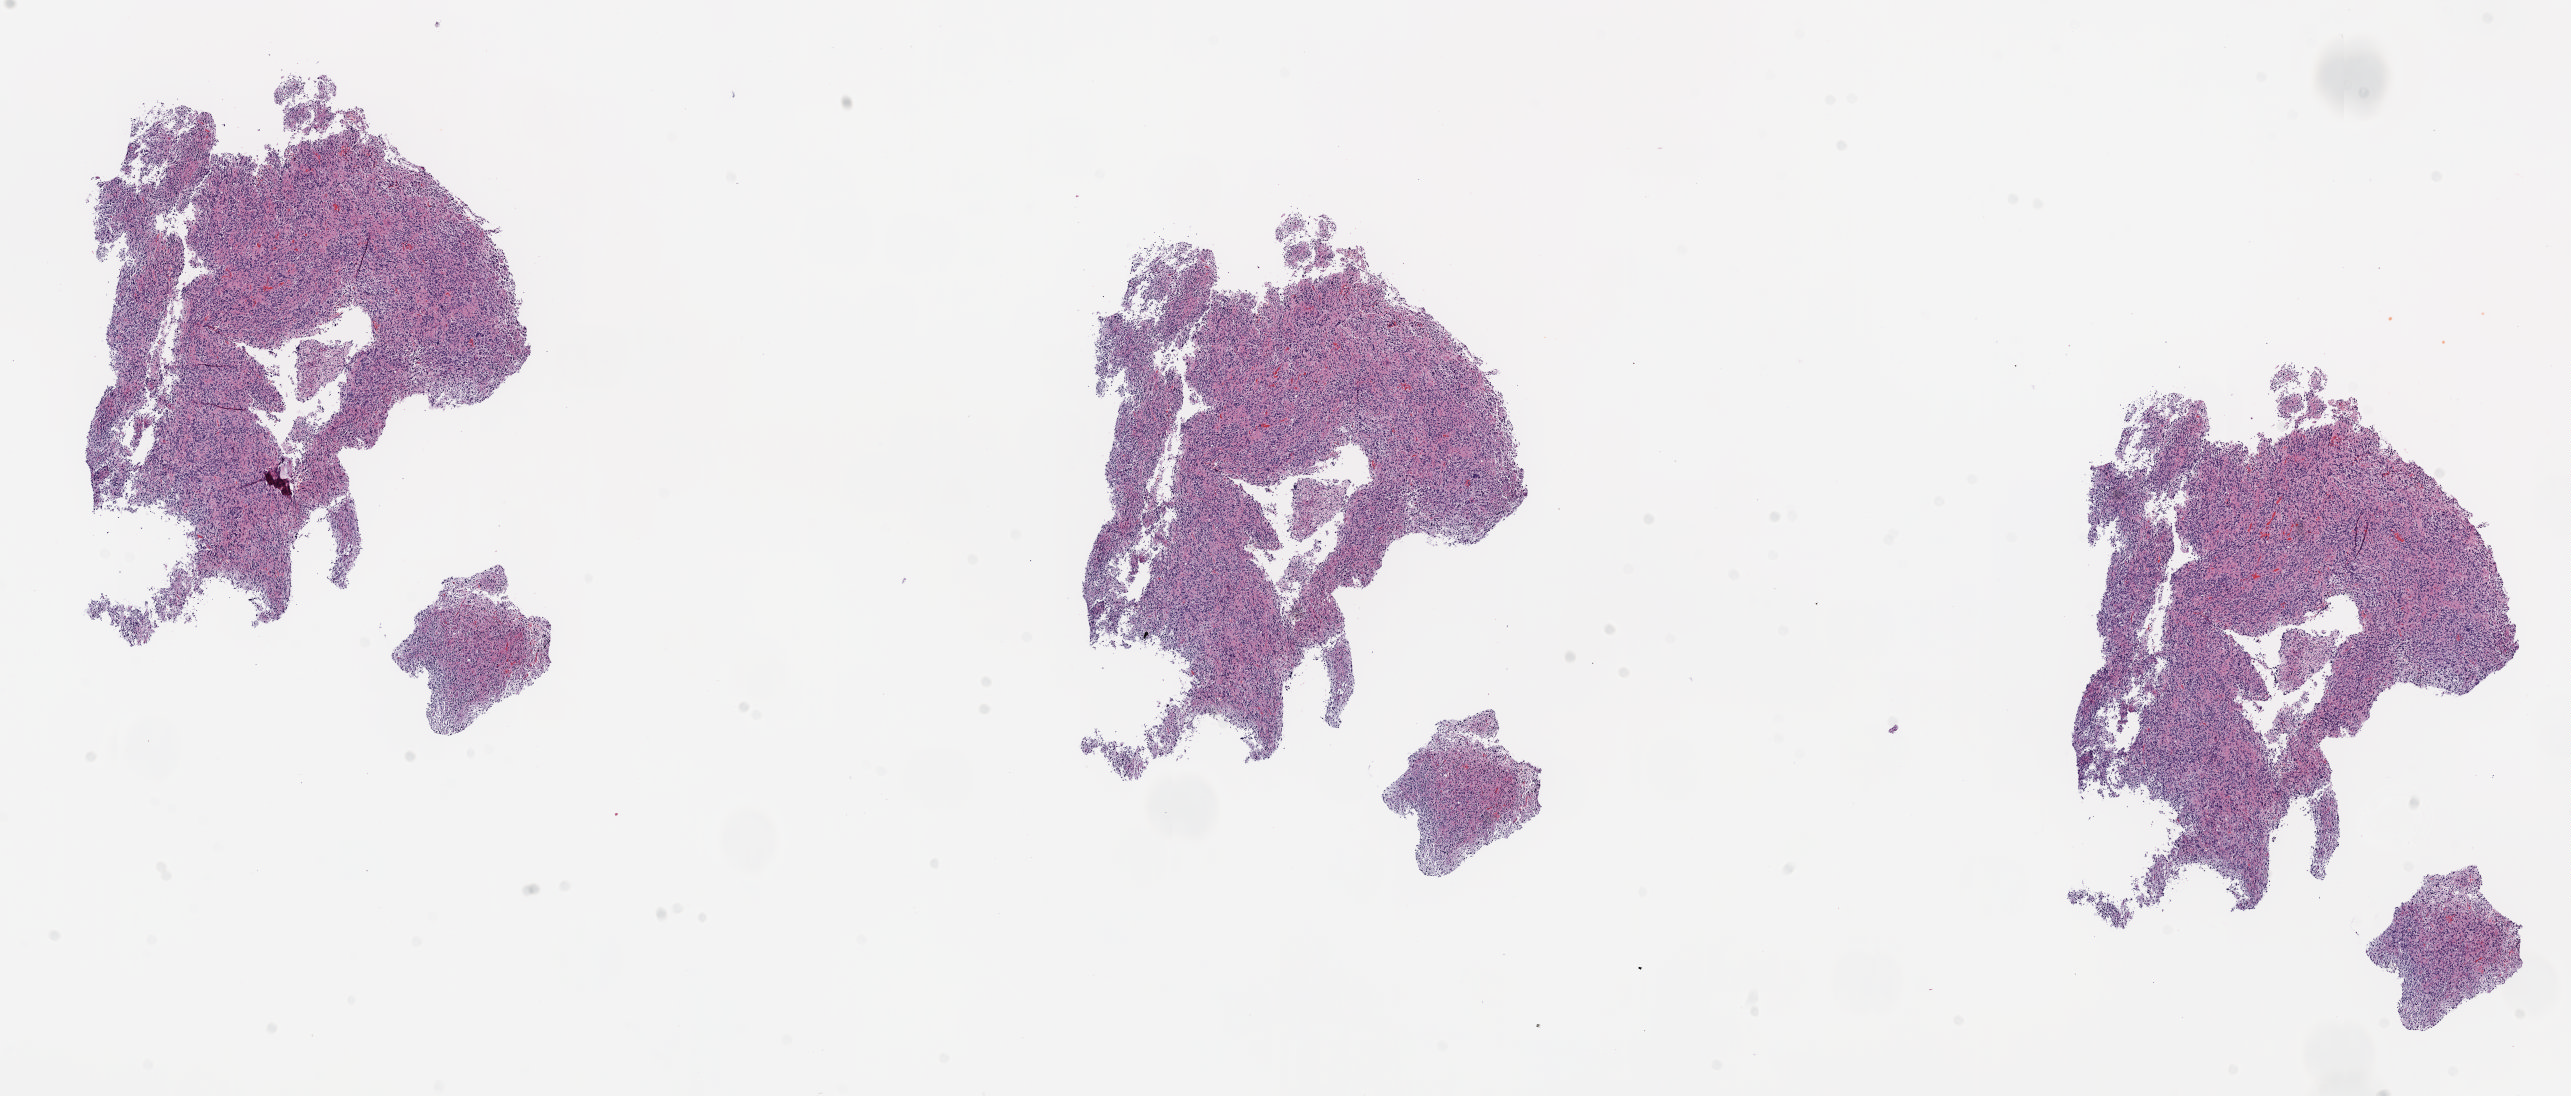
Digitized H&E-stained tissue section (whole slide), a low-resolution overview of the entire scanned area, about 20.6 x 8.8 mm, frozen section from the top of the tissue portion, primary tumour sample from the brain. Female patient; age at initial diagnosis 45 years. Slide review estimates, as recorded: tumour cells 100%, tumour nuclei 85%, normal cells 0%, stromal cells 0%, necrosis 0%.
Histologic diagnosis: Glioblastoma.